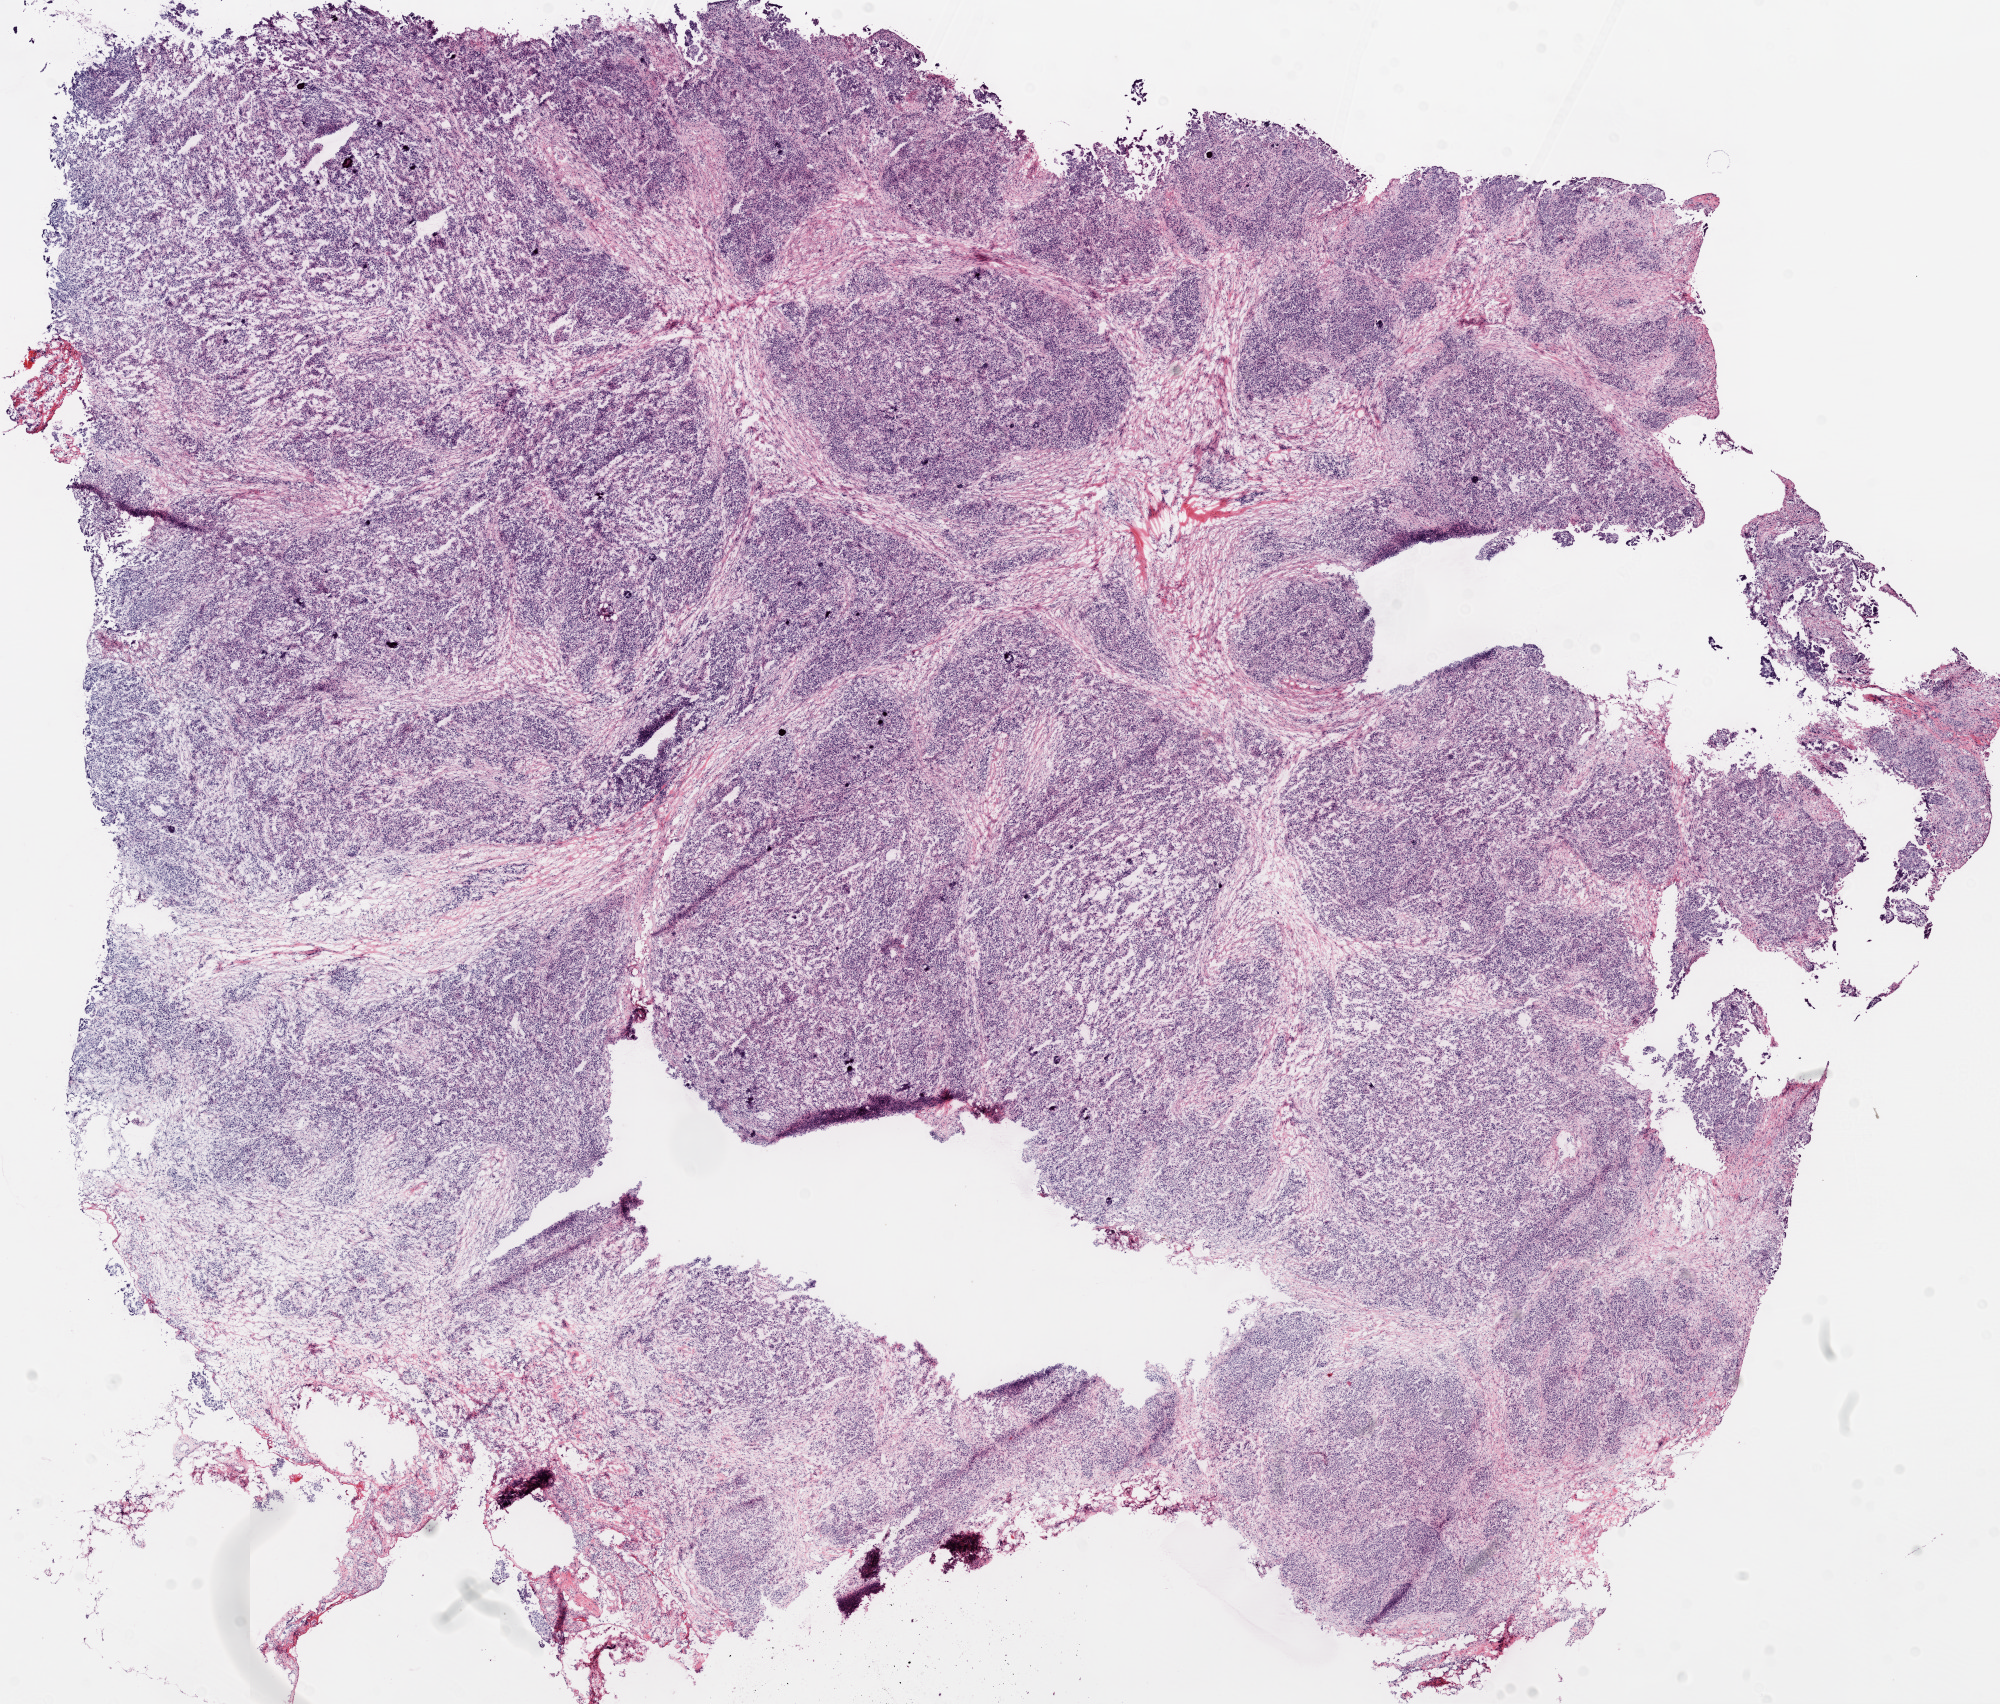
Digitized H&E-stained tissue section (whole slide), whole scanned area (about 16.0 x 13.7 mm) shown as a low-resolution overview, frozen section from the top of the tissue portion, primary tumour sample from the ovary. Female patient; age at initial diagnosis 81 years. Histologic grade: G3 (poorly differentiated). Slide review estimates, as recorded: tumour cells 89%, tumour nuclei 90%, normal cells 0%, stromal cells 10%, necrosis 1%.
FIGO stage: IIIC. Pathologic diagnosis: Serous cystadenocarcinoma, NOS.